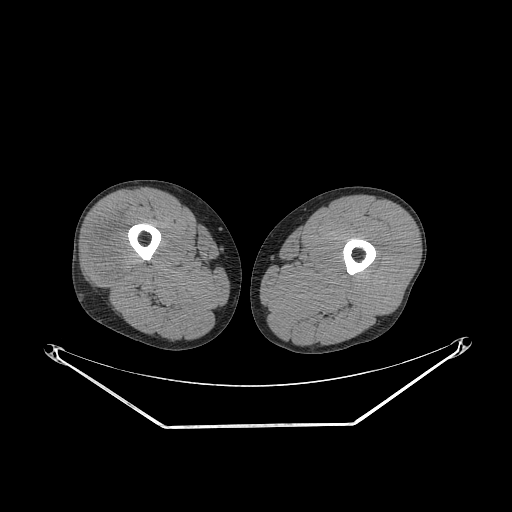
CT of an extremity soft-tissue mass (from a PET/CT study), one axial slice. Slice 231 of 267 in the series (ordered by position). 140 kVp. Soft-tissue window (W 400 / L 40 HU). 512 × 512 image matrix, field of view 500 × 500 mm. Male patient. Case-level facts recorded for this patient, not image findings: histological type: poorly differentiated synovial sarcoma; grade: high; site of the primary tumour: right buttock.
Outlined on this slice (expert contour drawn on MRI and transferred to this co-registered scan by the dataset authors):
- gross tumour volume including surrounding oedema: box from (x=89, y=228) to (x=143, y=284) px
- gross tumour volume (mass): (x=91, y=230)–(x=129, y=280)